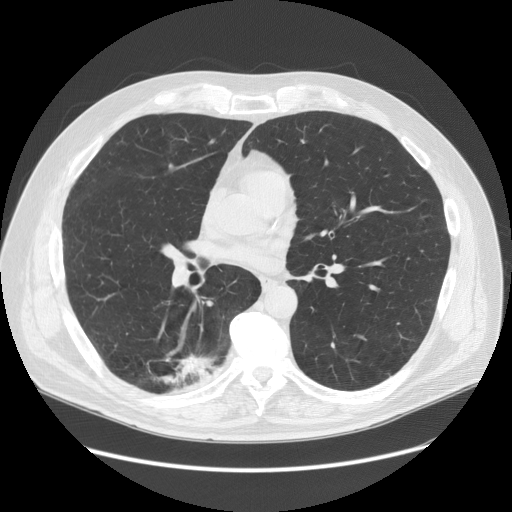
Low-dose screening chest CT, one axial slice; slice 74 of 149 in the series (ordered by position); lung window (W 1500 / L -600 HU); 2.5 mm slice thickness; 512 × 512 image matrix, field of view 400 × 400 mm.
Annotated regions visible in this slice (outlined manually by an expert reader):
- lesion 1 (tumor, lower lobe of right lung): bounding box [x1, y1, x2, y2] px = [158, 354, 216, 386]